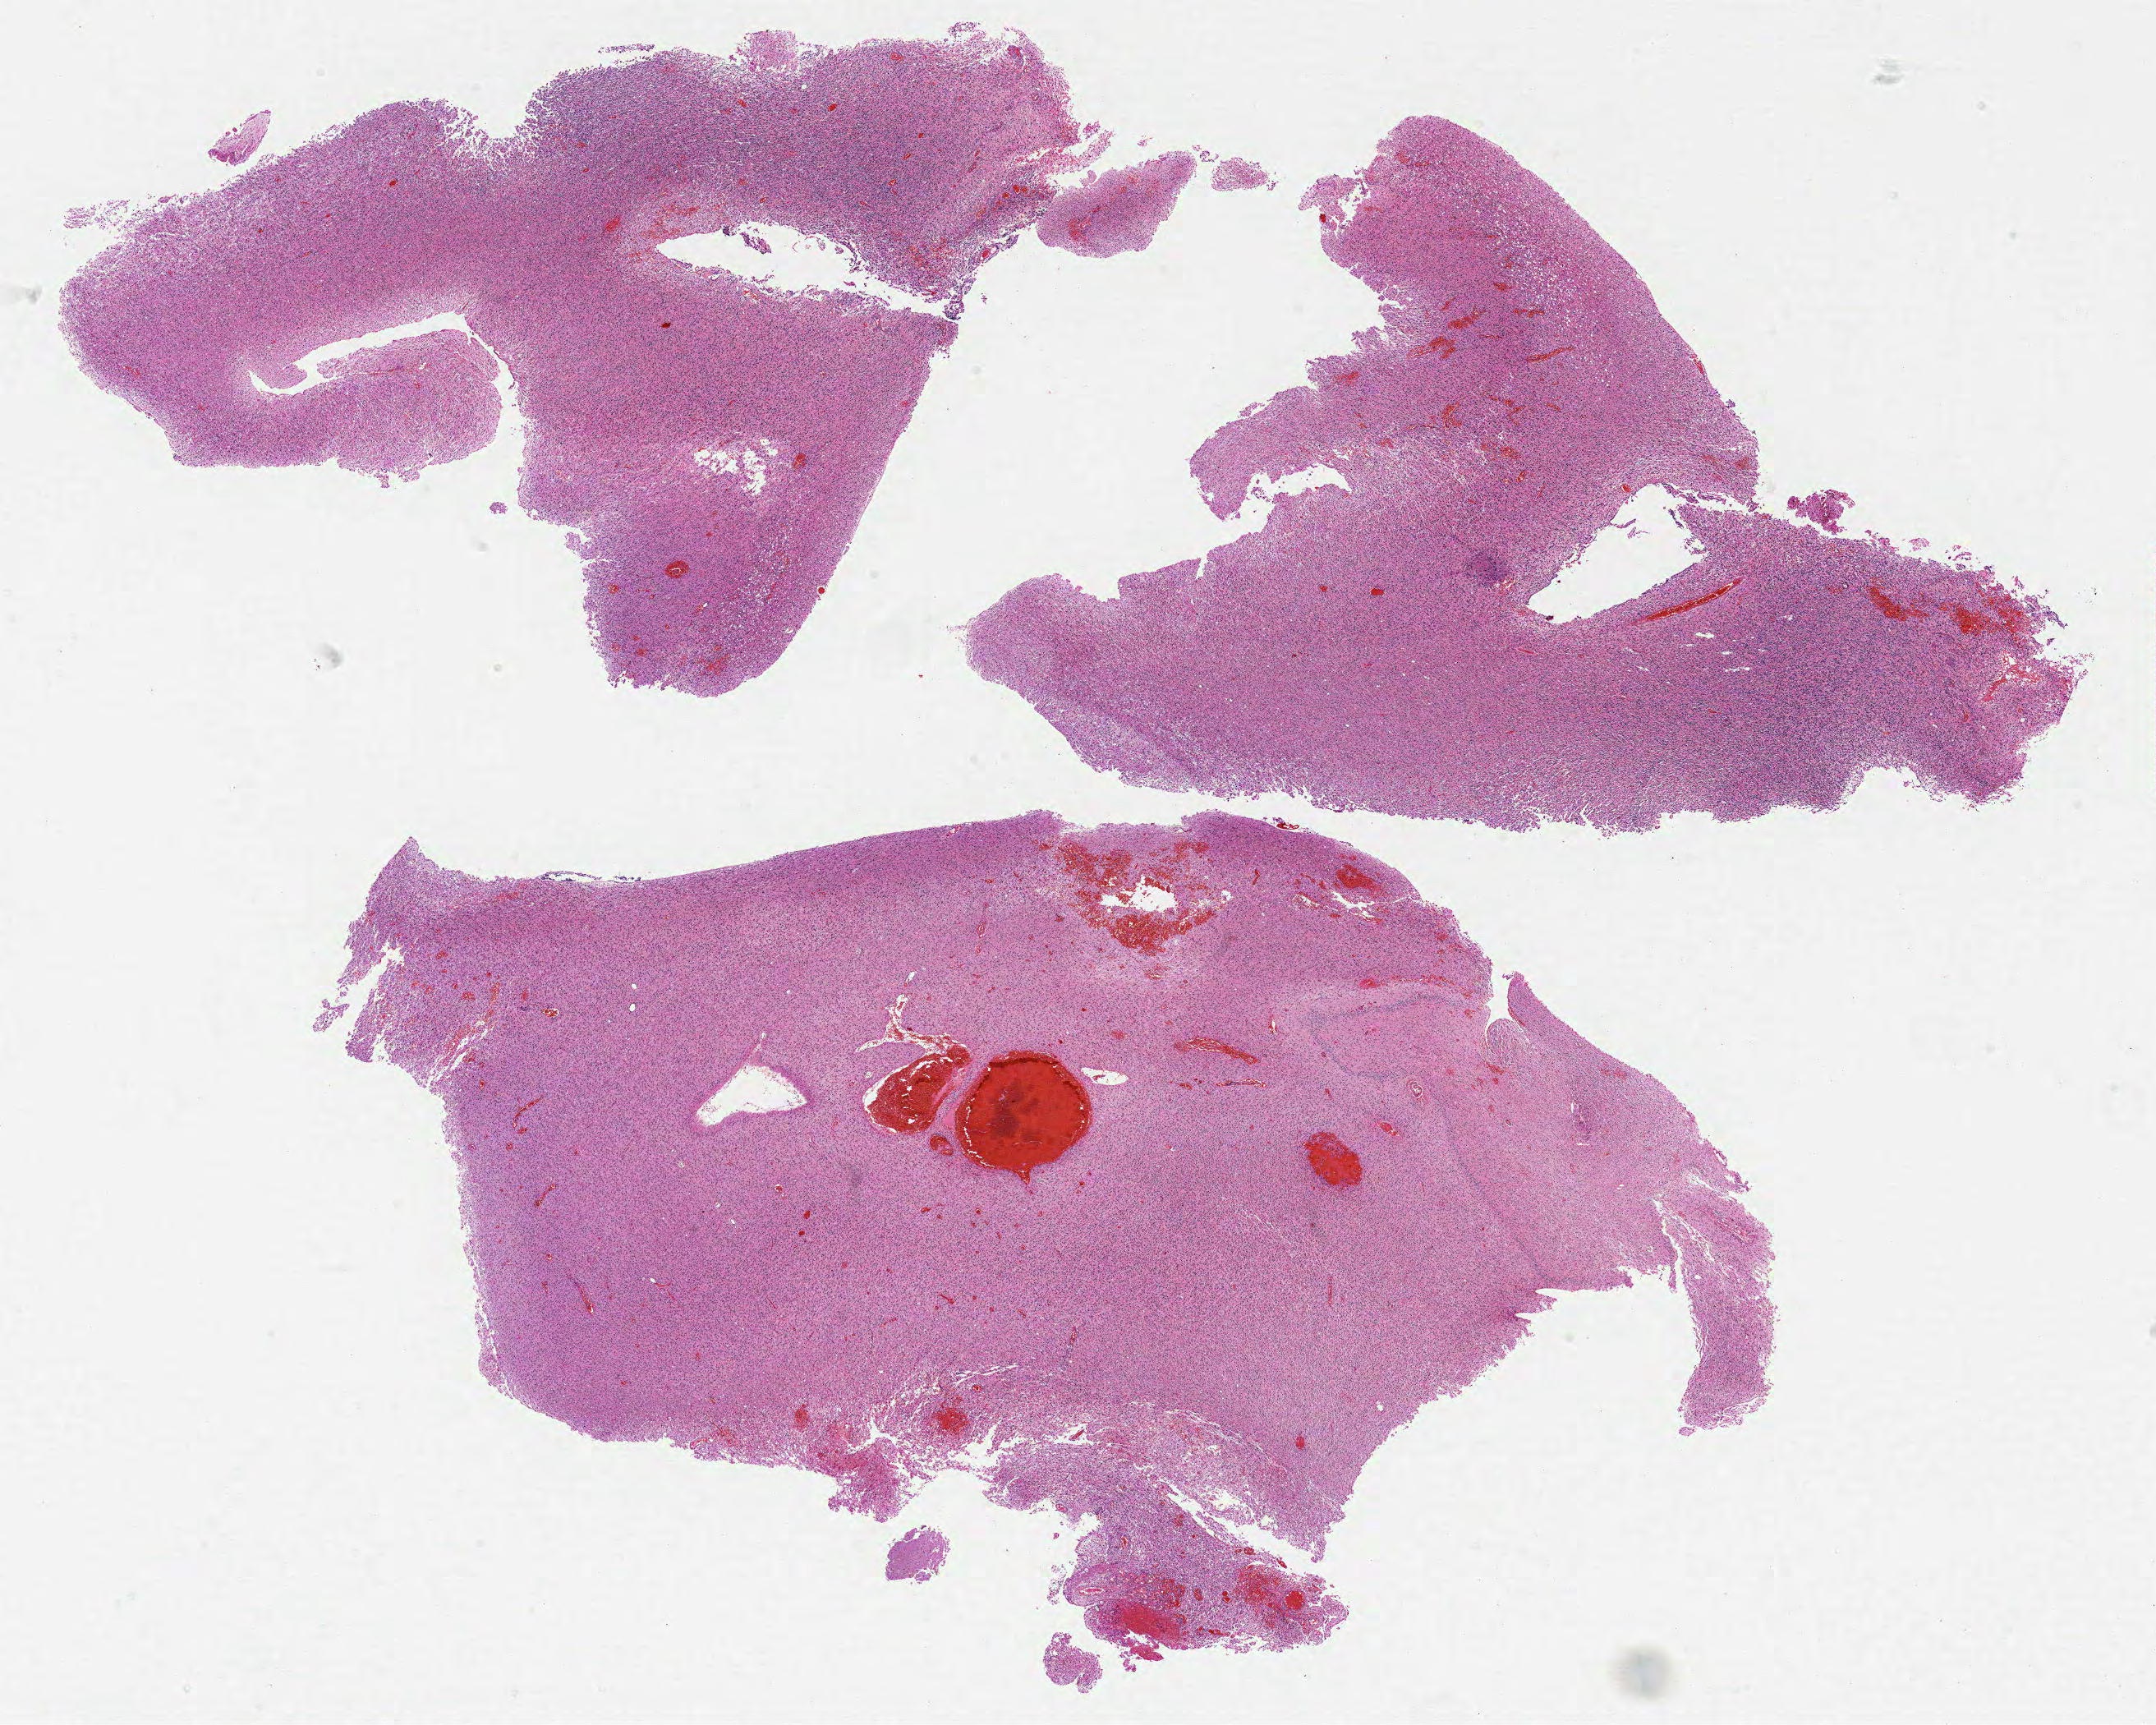
Hematoxylin and eosin (H&E) stained whole-slide image, whole scanned area (about 21.0 x 16.8 mm, from a 20x scan) shown as a low-resolution overview, FFPE section, sample: primary tumour, brain. Patient: female, age at initial diagnosis 75 years.
- diagnosis: Glioblastoma